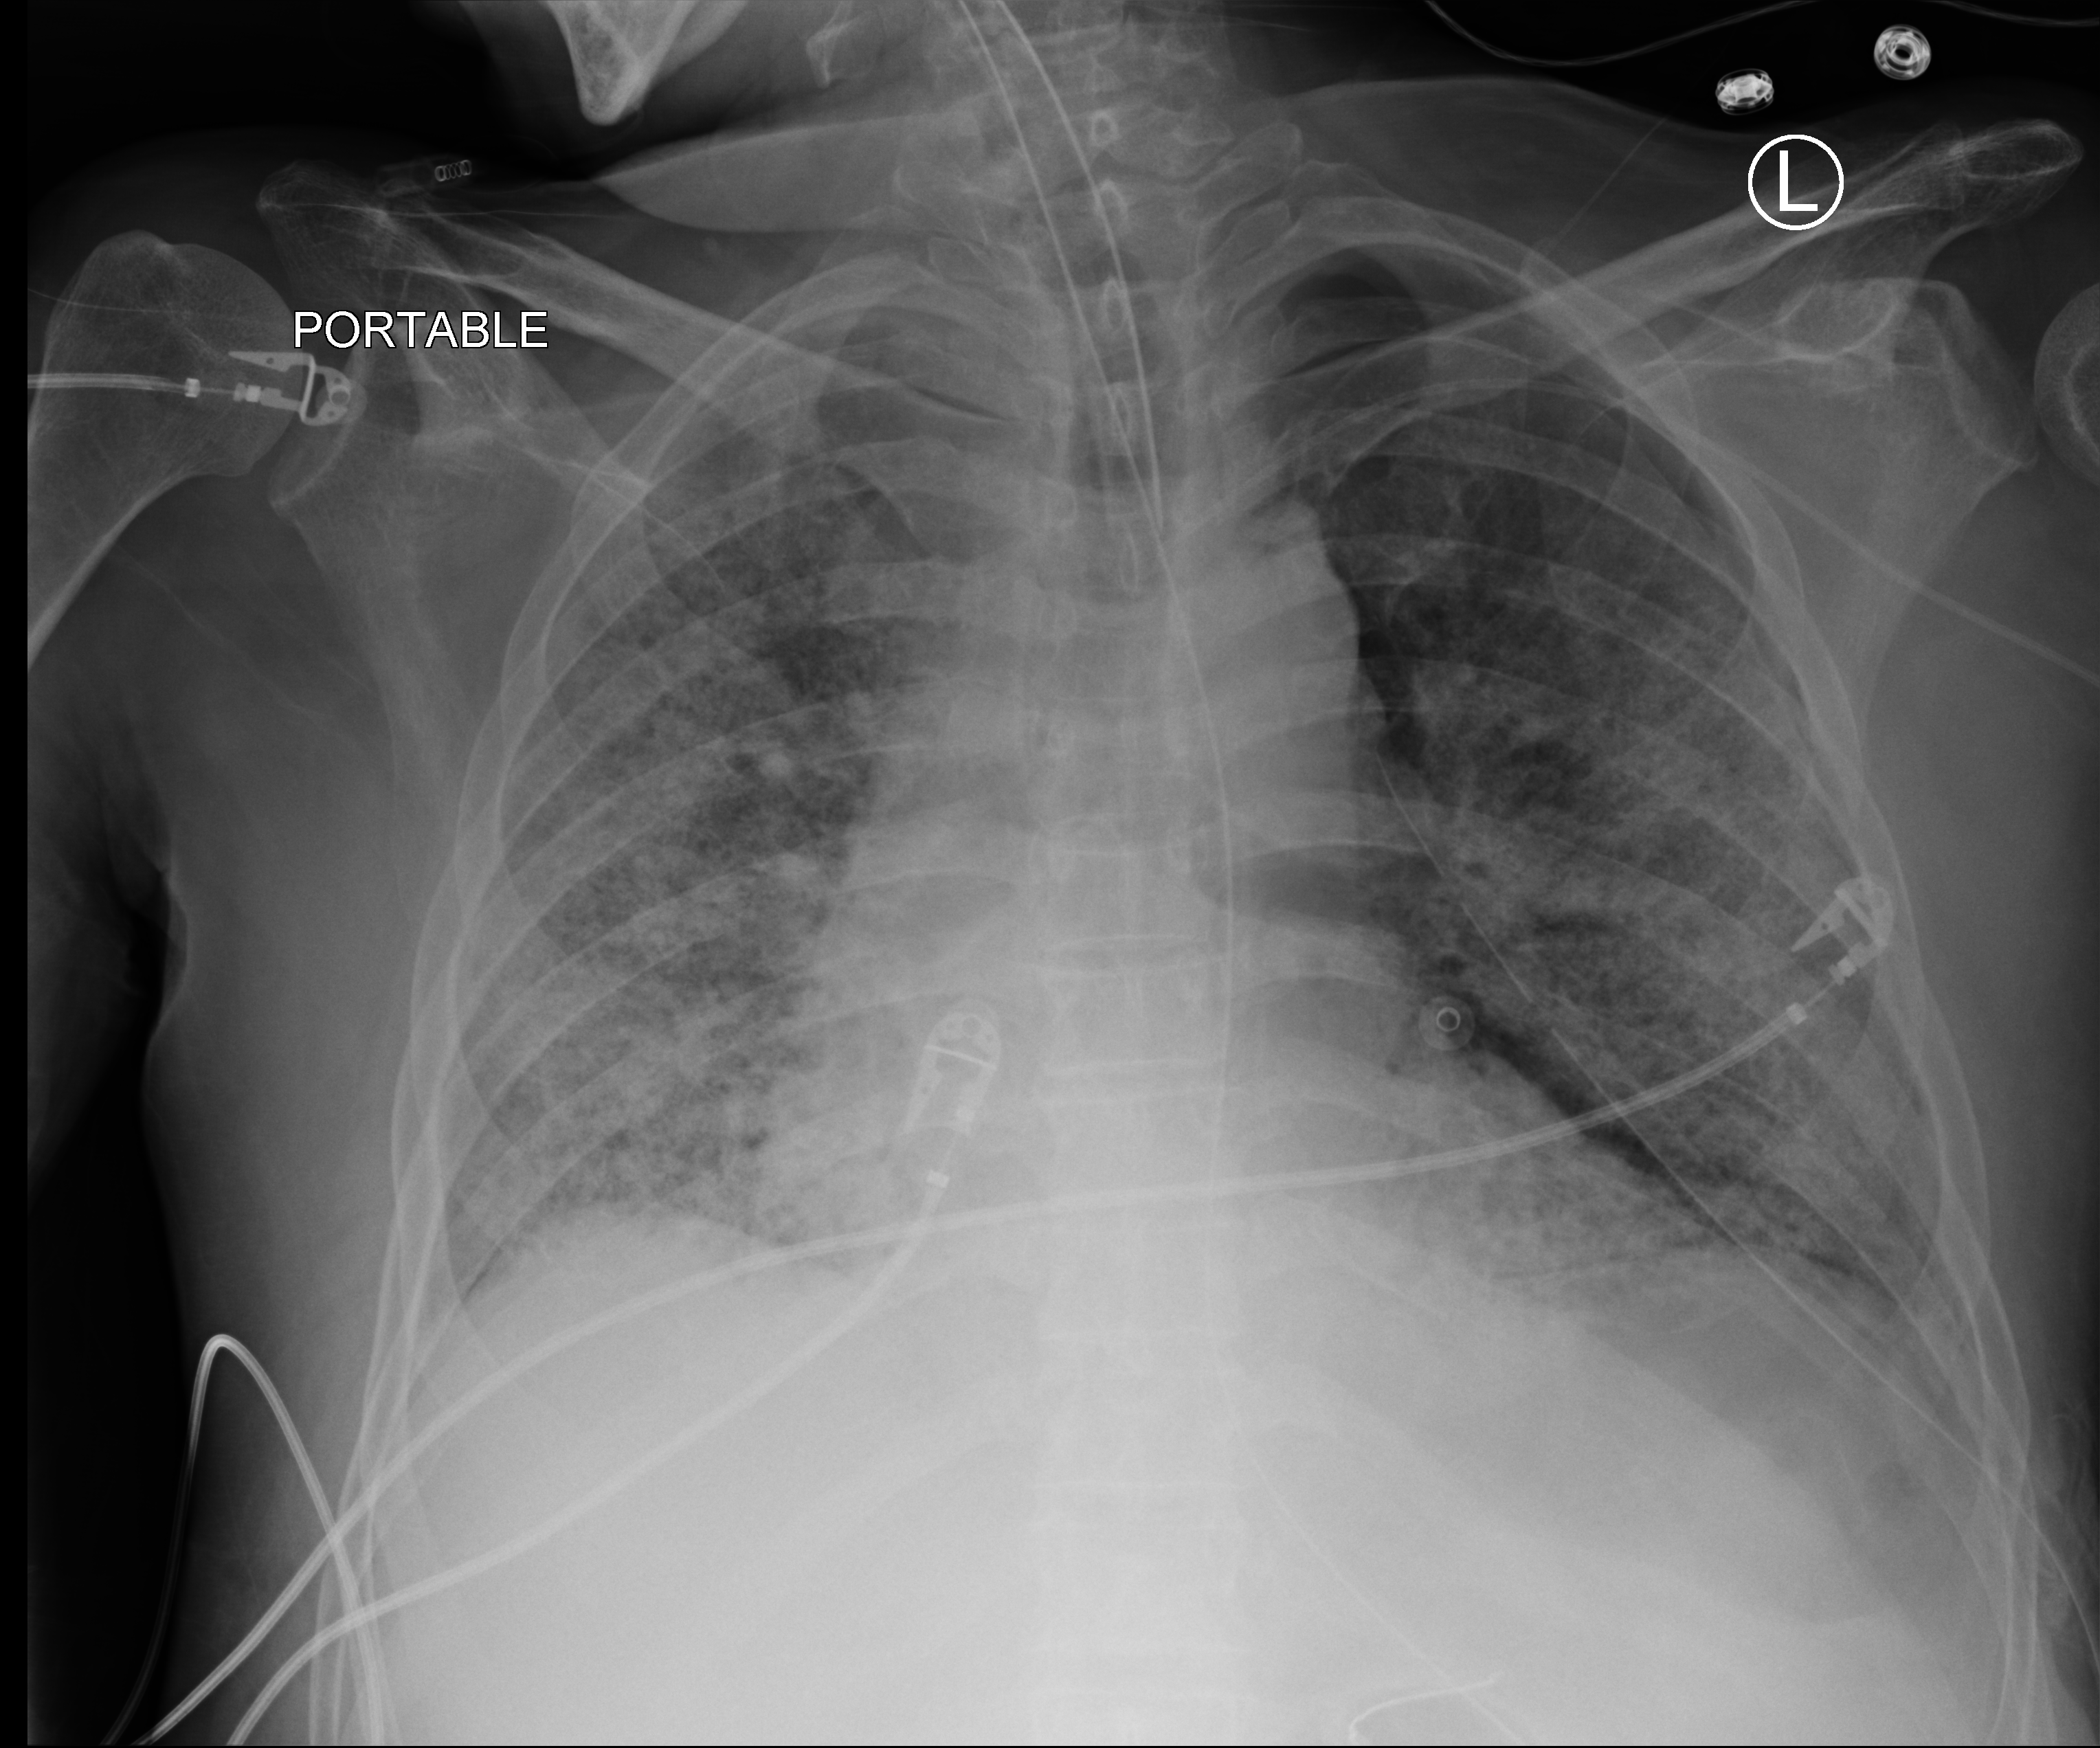
Chest X-ray (portable); anteroposterior (AP) projection. Patient hospitalised with COVID-19; male, aged 60–74 years.
From the hospital-stay record, not from the radiograph (when in the stay this image was taken is not recorded): mechanically ventilated during this hospital stay: yes.